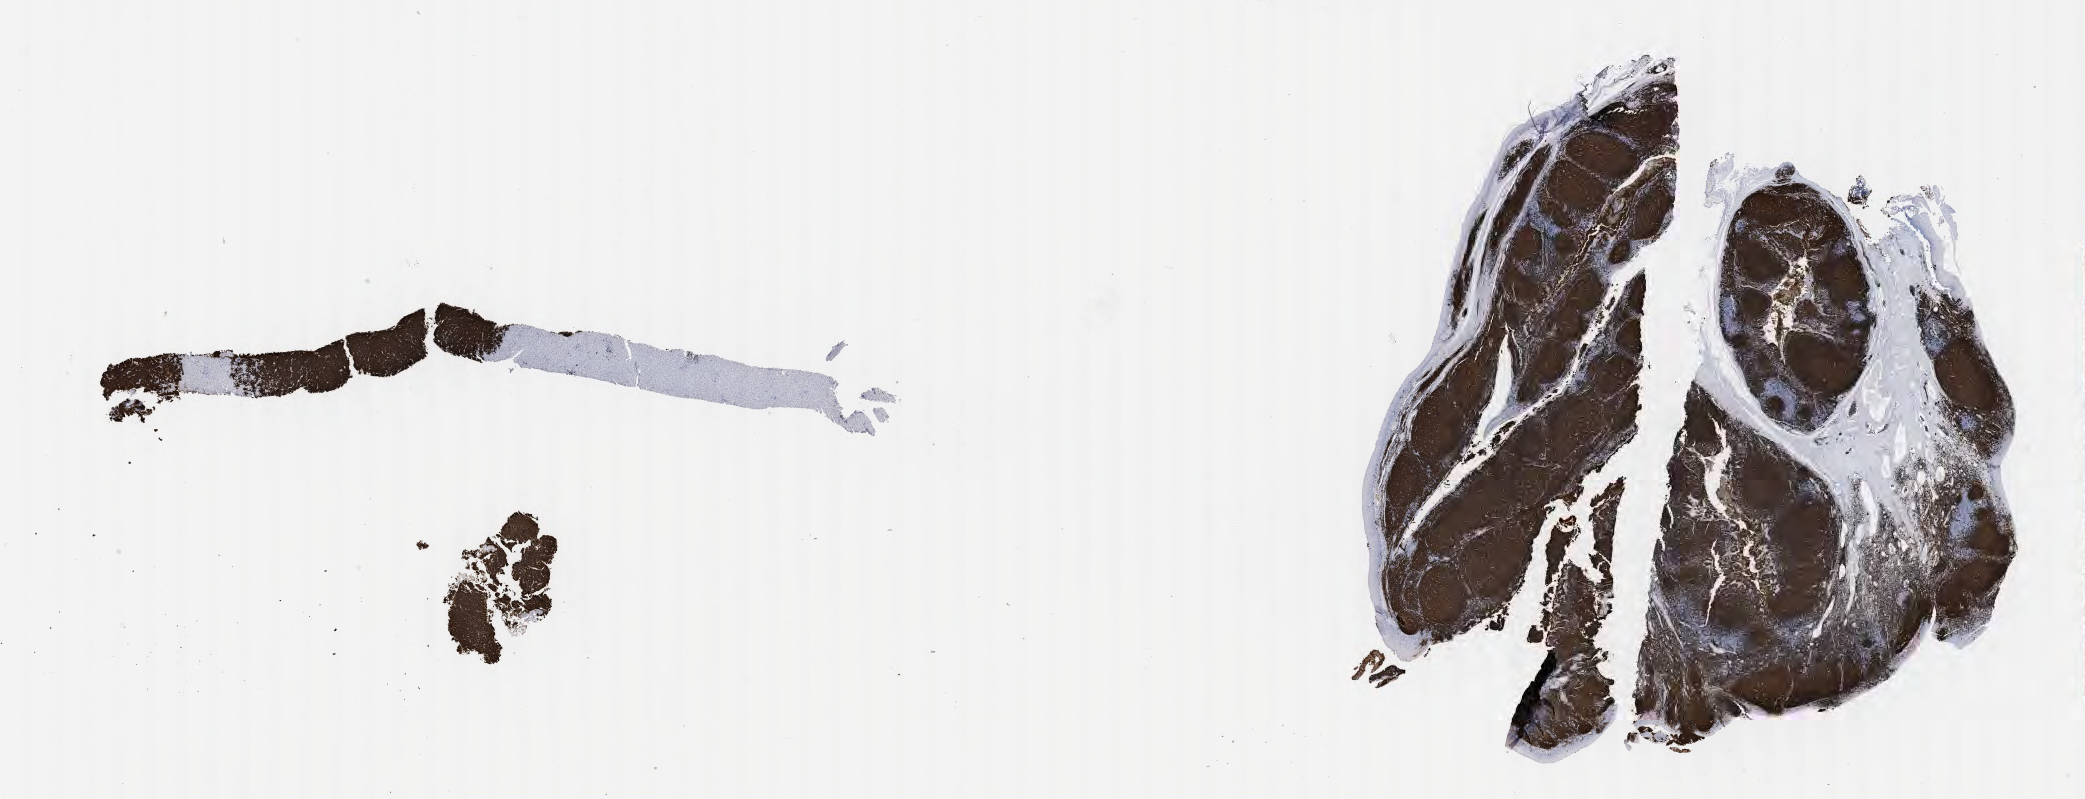
IHC for CD20, whole-slide image — whole scanned area (about 33.7 x 12.9 mm) shown as a low-resolution overview, specimen: tumor tissue. Patient: male, age 68 years.
- histologic diagnosis: Burkitt lymphoma, NOS